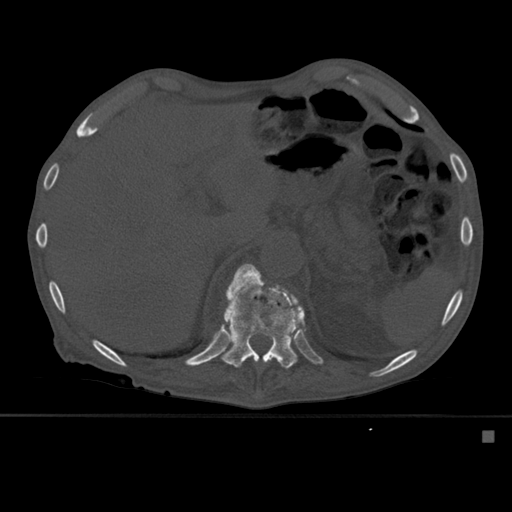
CT including the spine, one axial slice; position 281 of 527 along the scan axis; bone window (W 1800 / L 400 HU); 512 × 512 image matrix, field of view 373 × 373 mm. Male patient, age 78 years. From the clinical record (not read from this slice): primary cancer: prostate.
Outlined on this slice (semi-automatic segmentation, software-assisted and operator-edited):
- T11 vertebra: box from (x=220, y=264) to (x=294, y=369) px
- T12 vertebra: (x=221, y=268)–(x=305, y=365)
- T9 vertebra: (x=227, y=352)–(x=229, y=359)